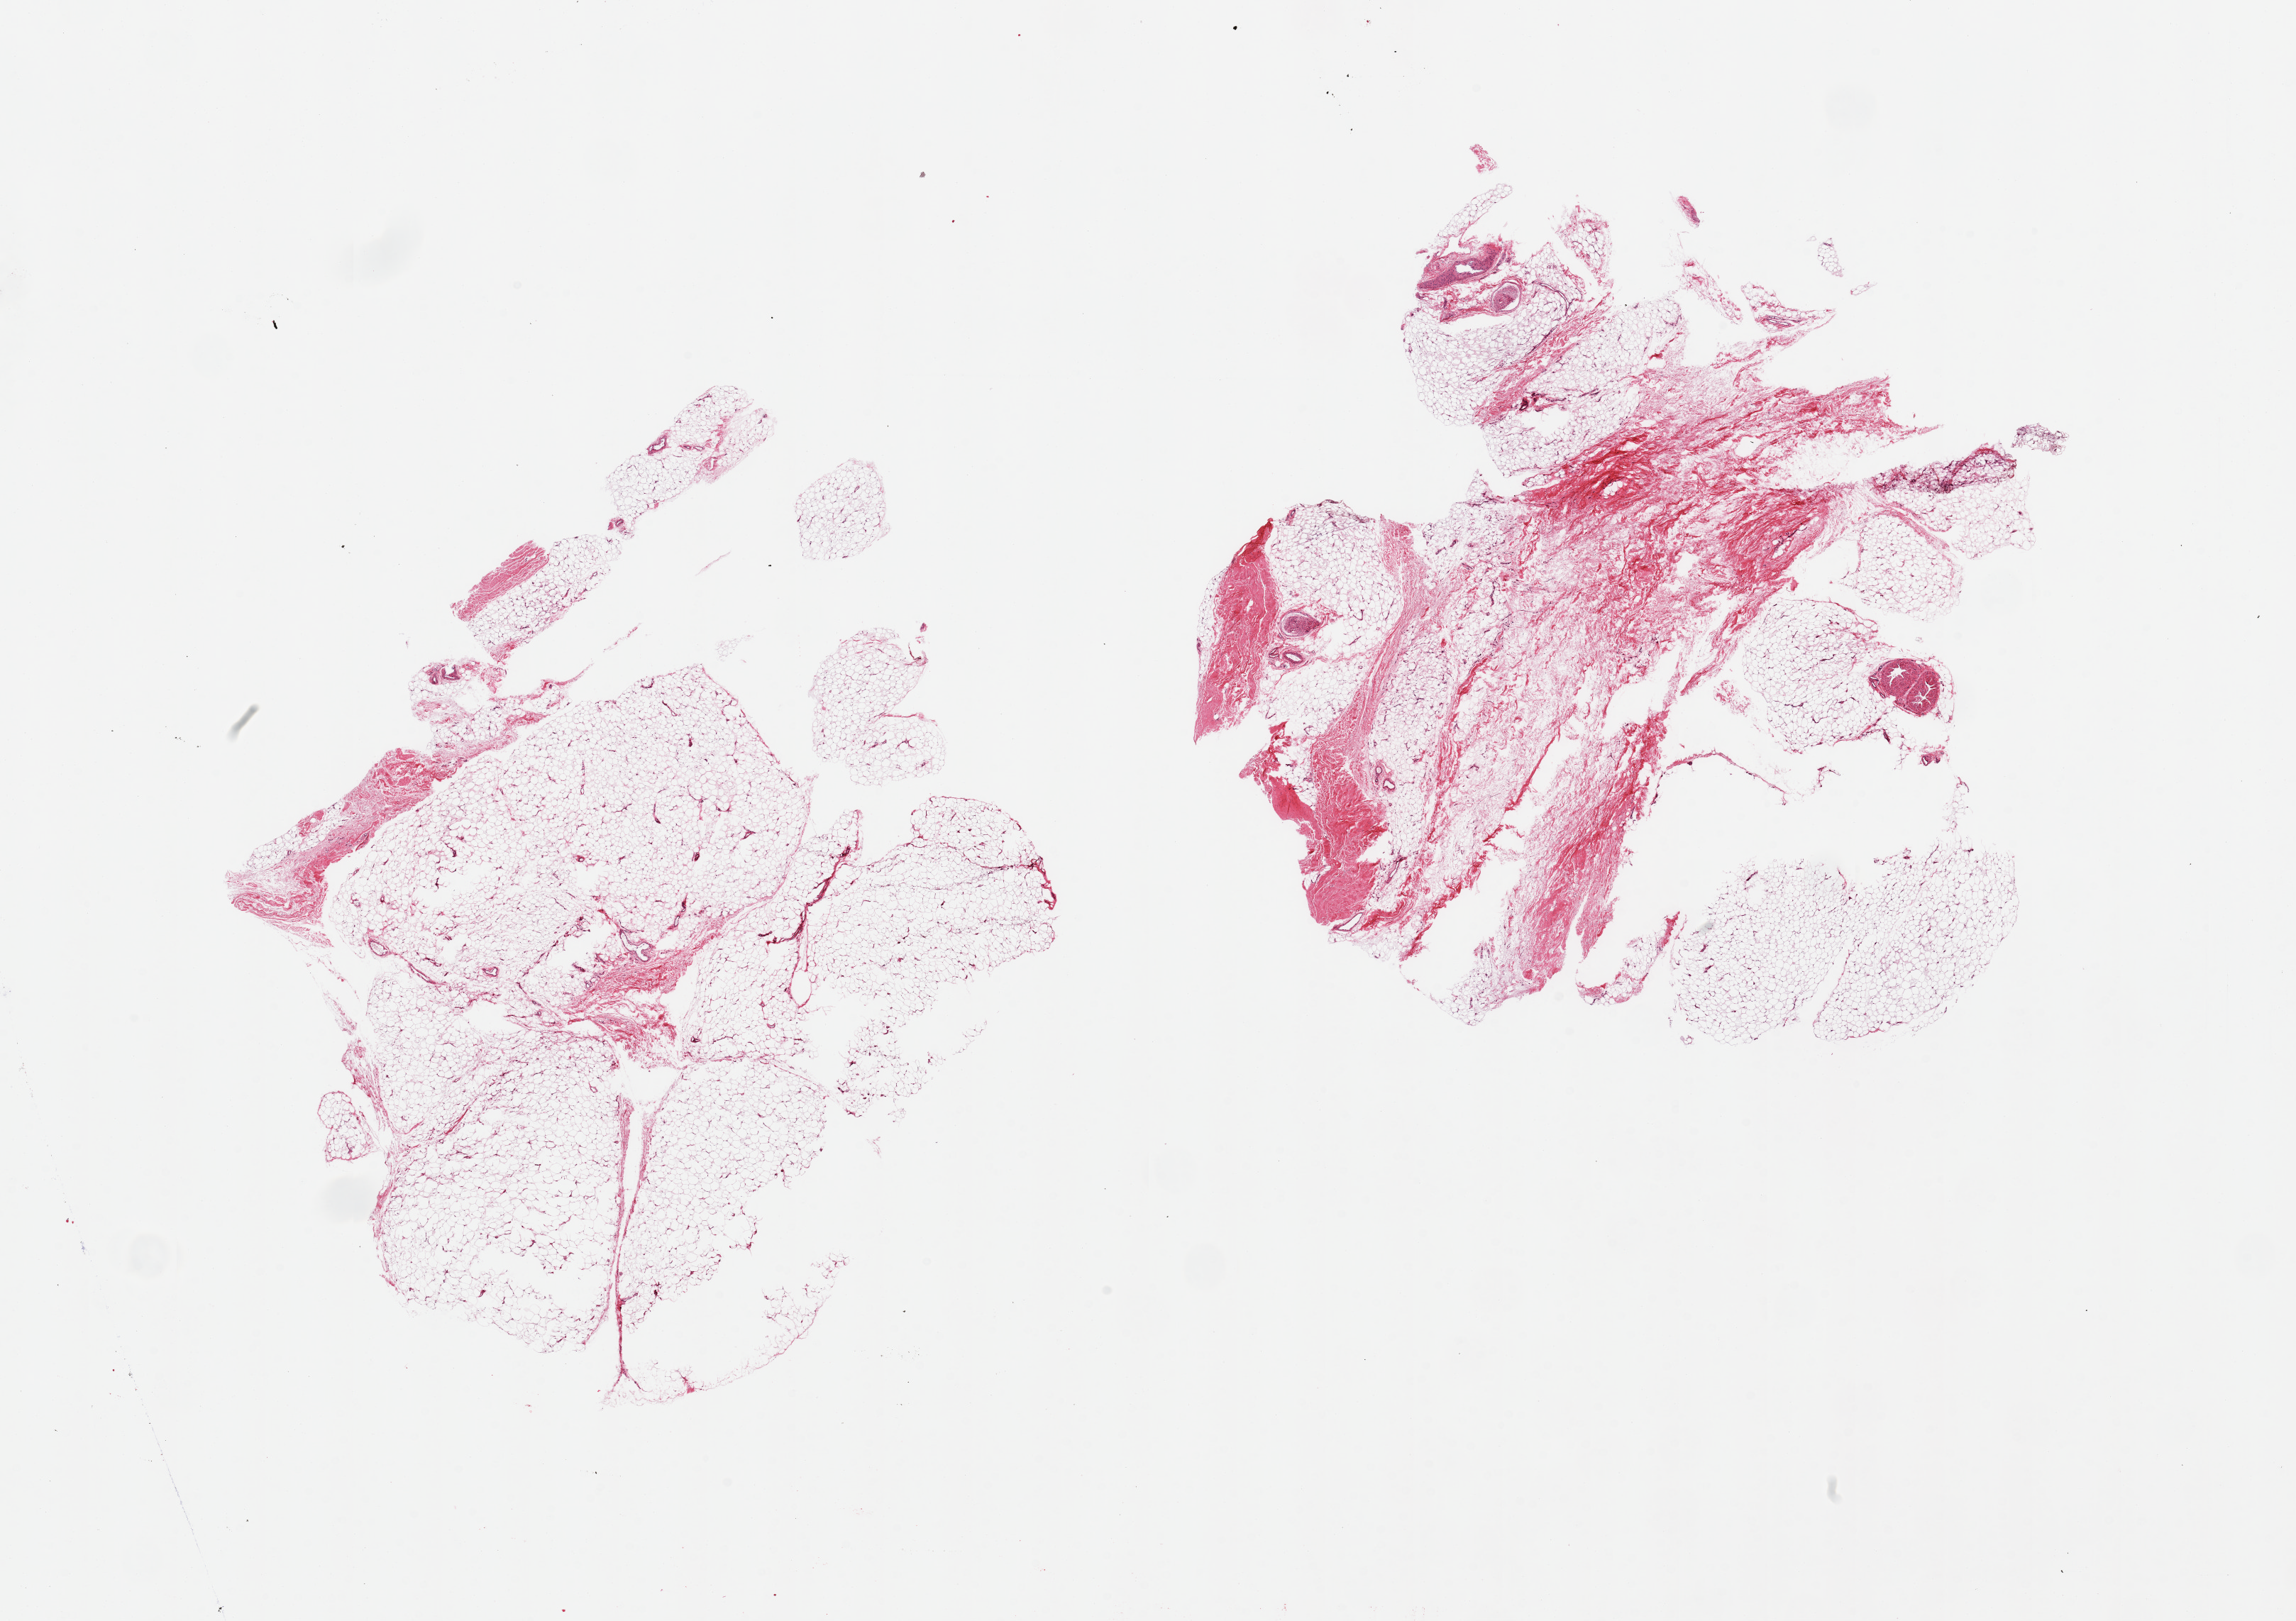
Haematoxylin and eosin whole-slide image, brightfield, whole scanned area (about 25.6 x 18.1 mm) shown as a low-resolution overview, PAXgene-fixed, paraffin-embedded tissue, target tissue: adipose tissue, tissue donor sample. Male donor.
• pathologist's review note for this sample: 2 pieces; 20% internal fibrous content in 1 piece; 5% in other